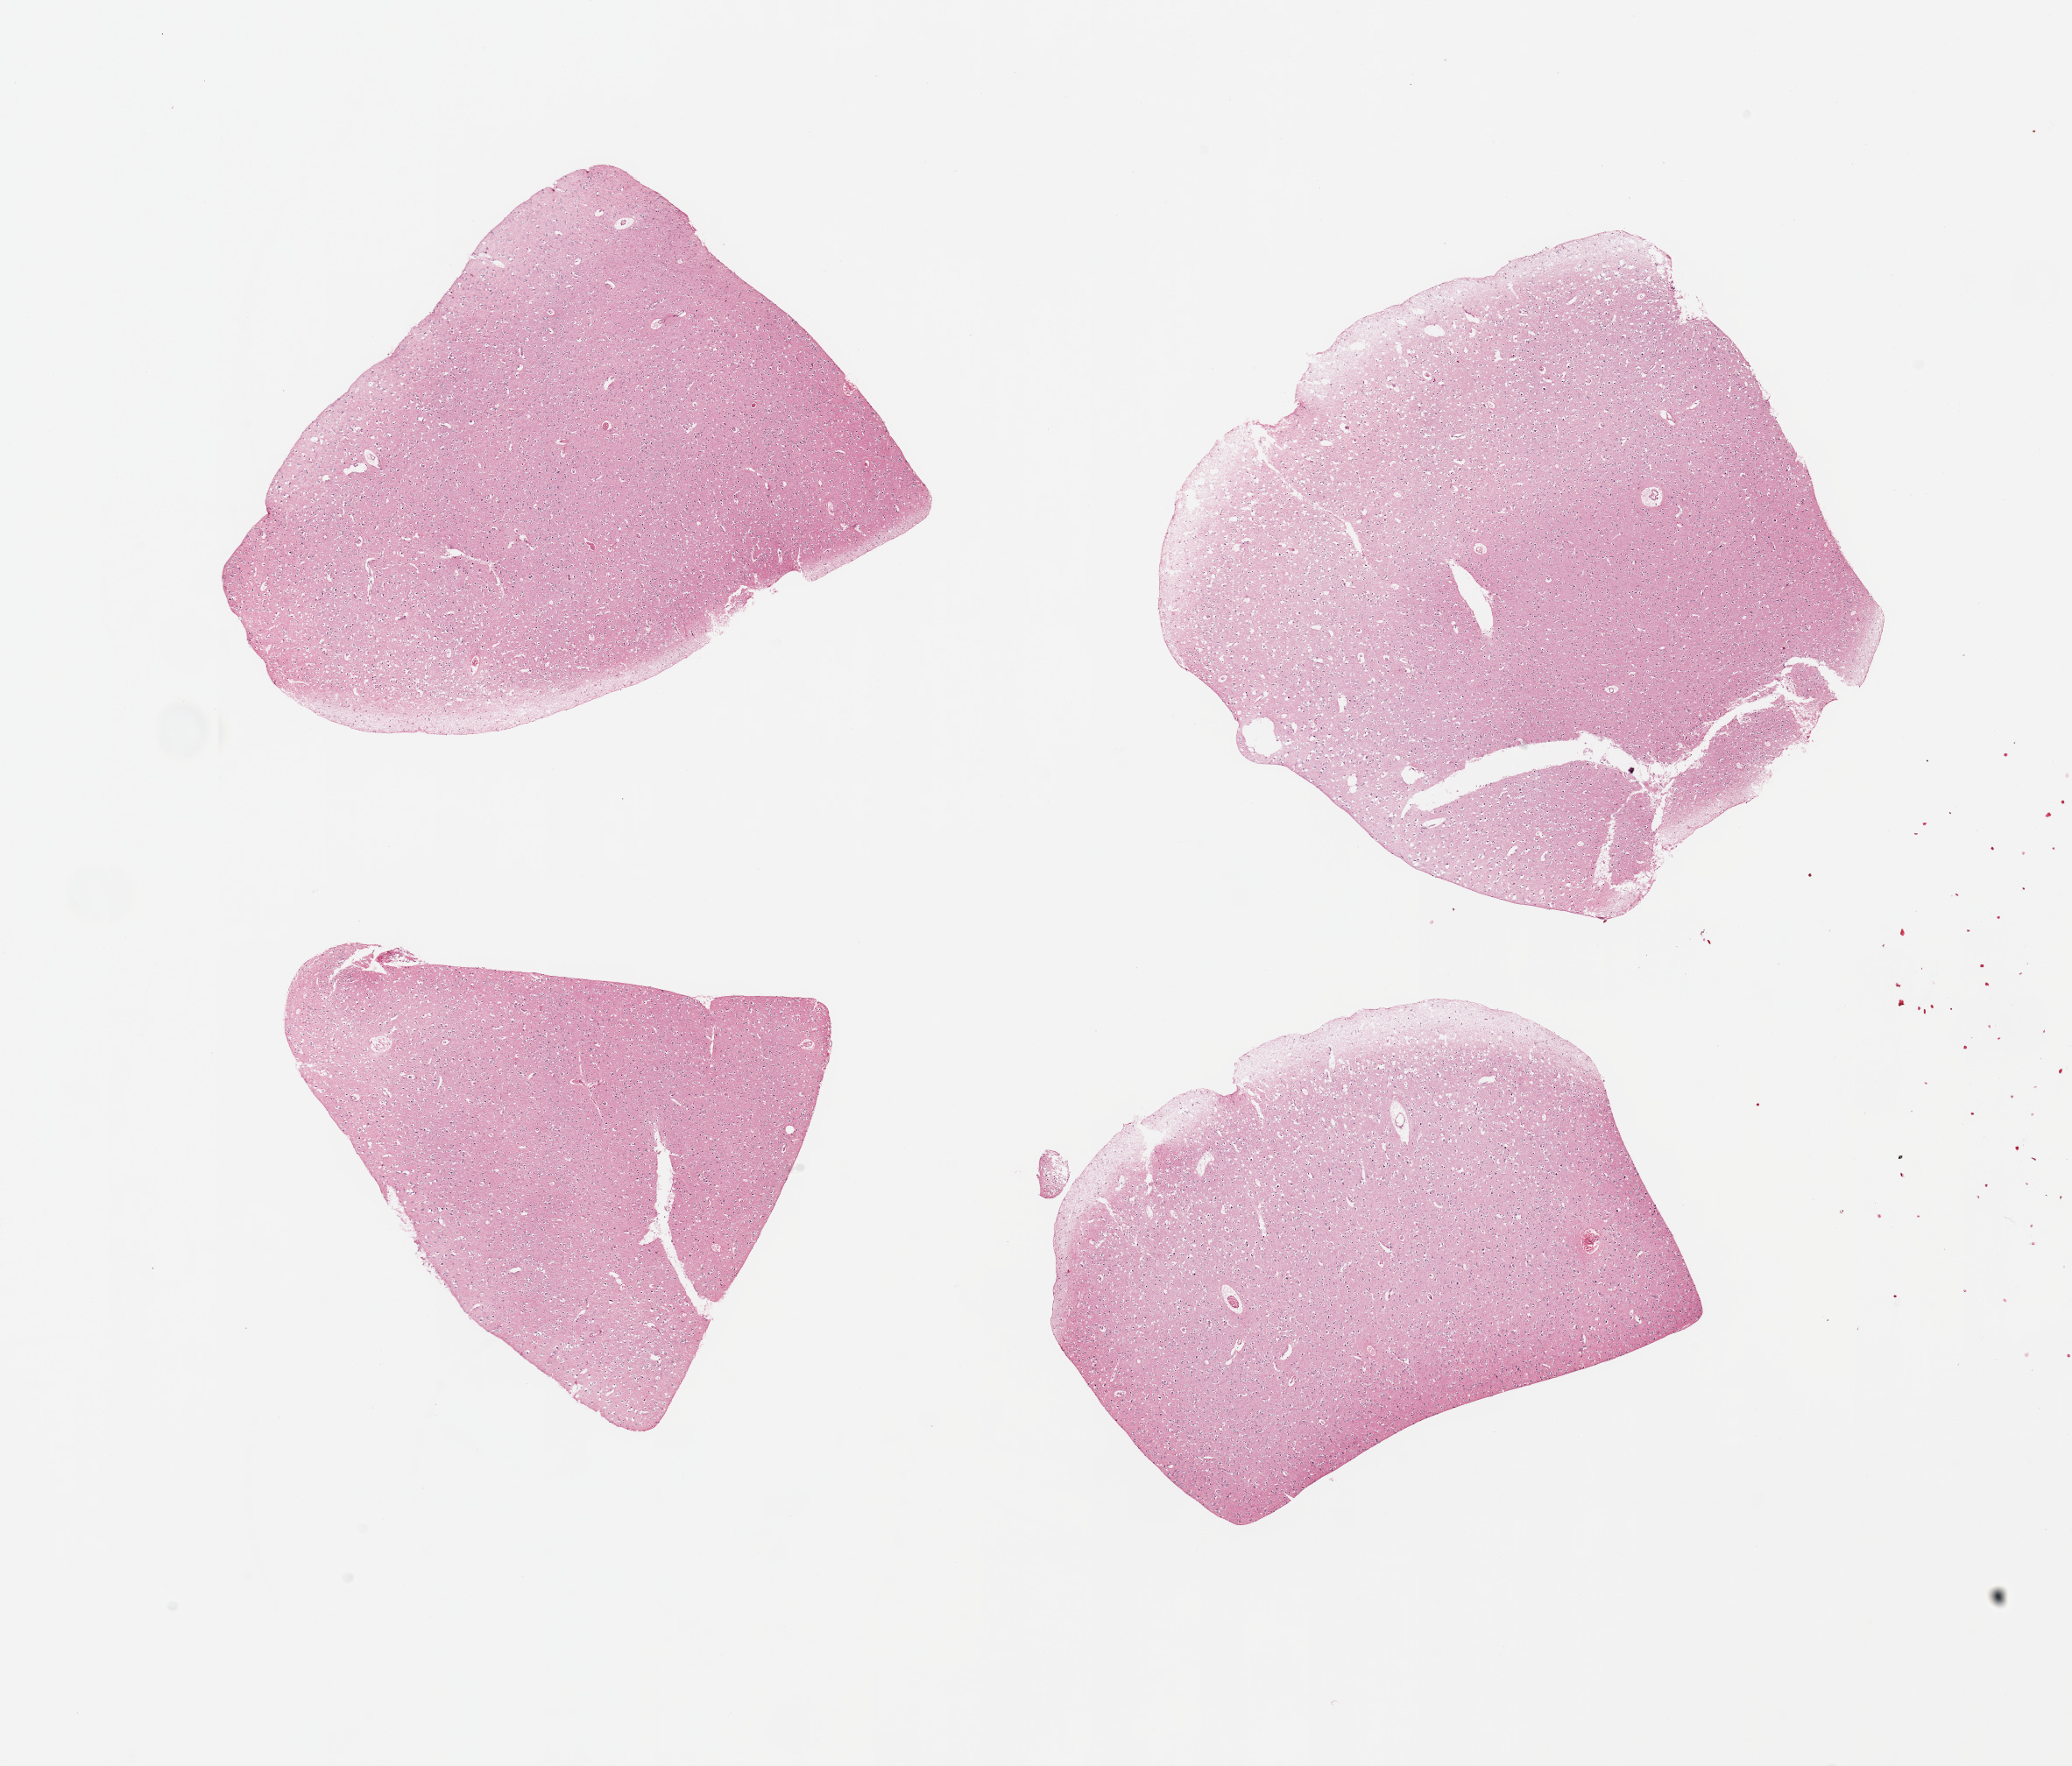
Digitized haematoxylin and eosin-stained section, shown as a low-resolution overview of the whole scanned area (about 18.7 x 15.9 mm, acquisition: 20x scan); PAXgene-fixed, paraffin-embedded tissue; section of cerebral cortex (target tissue); donor tissue sample. Donor: male.
• review note (as recorded): 4 pieces, no abnormalities